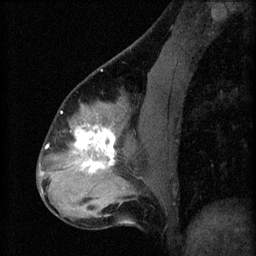
Breast MRI (dynamic contrast-enhanced), one sagittal slice. Slice 27 of 60 in the series (ordered by position). 3 images stored at this slice position (order not interpretable as contrast timing). 1.5 T. TE 4.2 ms, TR 8.2 ms. 2.3 mm slice thickness. 256 × 256 image matrix. Female patient, age 37 years.
Annotated regions visible in this slice (semi-automatic segmentation, software-assisted and operator-edited):
- analysis volume of interest (the breast-tissue region the enhancement analysis was run in; not a lesion): bounding box (x1, y1, x2, y2) in pixels: (67, 120, 122, 179)
- tumour enhancement mask (voxels above the 70 % enhancement threshold inside the analysis volume of interest): (74, 124, 116, 173)